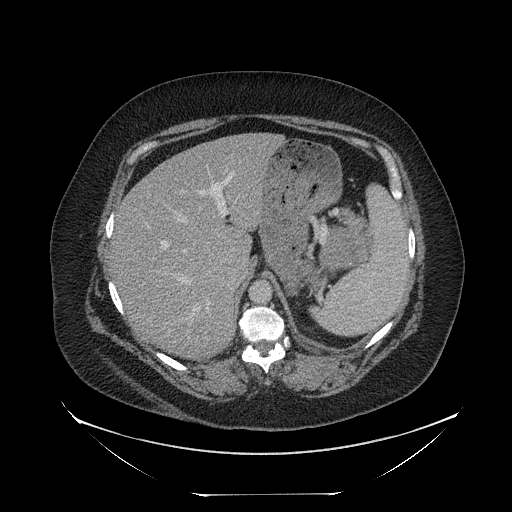
Contrast-enhanced abdominal CT, one axial slice; position 166 of 205 along the scan axis; 120 kVp; intravenous contrast given; soft-tissue window (W 400 / L 40 HU); 2.5 mm slice thickness; 512 × 512 image matrix, field of view 500 × 500 mm. Female patient, age 53 years. Case-level facts recorded for this patient, not image findings: diagnosis: adrenocortical carcinoma; tumour side: left adrenal; tumour size at pathology: 17 cm; Ki-67 index: 20 %; stage (as recorded): 3.
Annotated regions visible in this slice (semi-automatic segmentation, software-assisted and operator-edited):
- mass: bounding box [x1, y1, x2, y2] px = [323, 229, 365, 266]